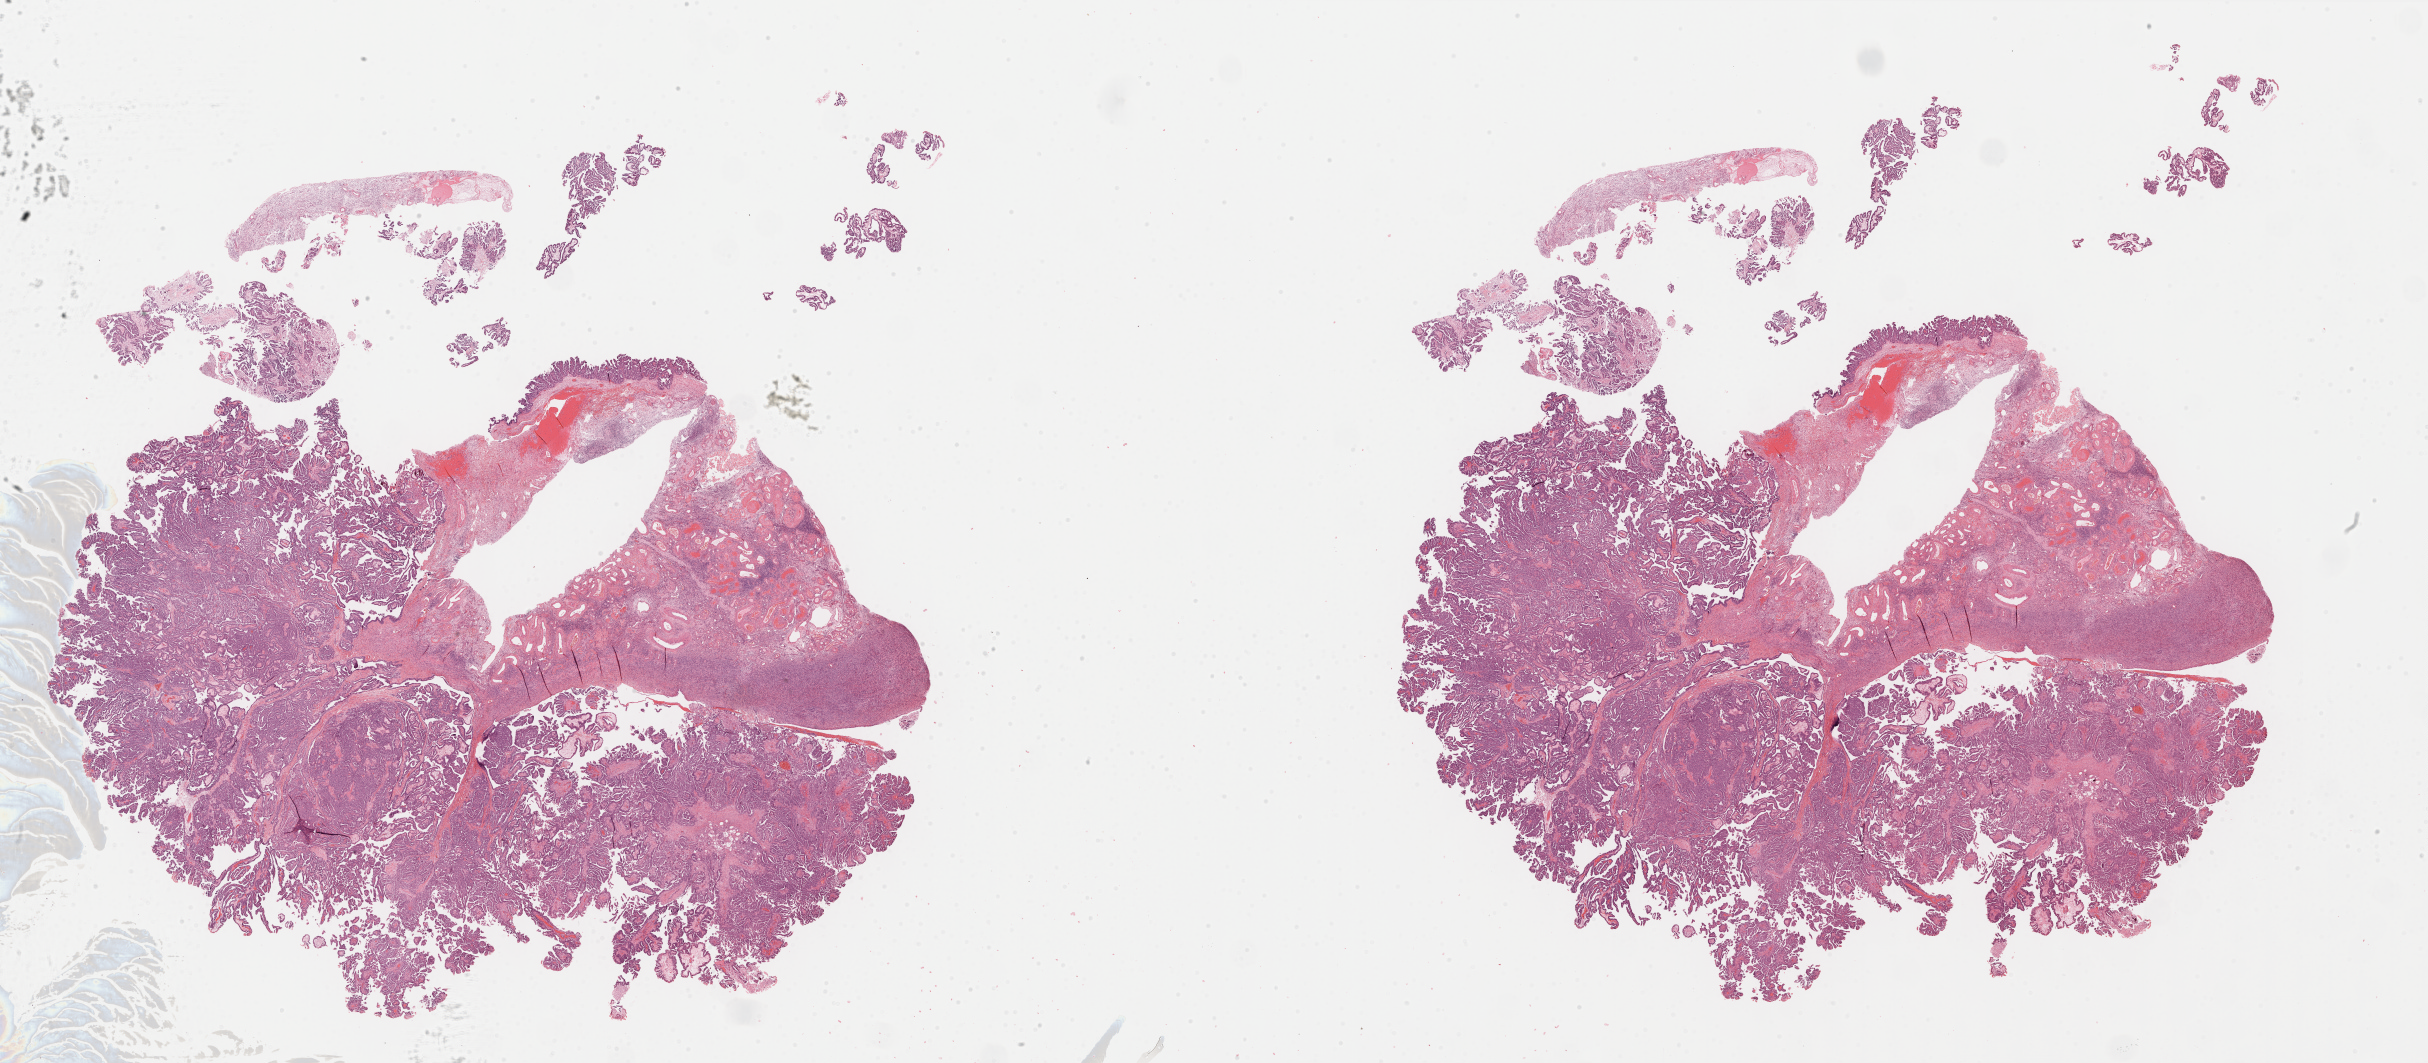
Digitized H&E tissue section (whole slide) — a low-resolution overview of the entire scanned area, about 39.2 x 17.2 mm (from a 40x scan), formalin-fixed paraffin-embedded (FFPE) diagnostic section, ovary, primary tumour sample. Female patient; age at initial diagnosis 68 years. Histologic grade: G3 (poorly differentiated).
Pathologic diagnosis: Serous cystadenocarcinoma, NOS. FIGO stage: IV.